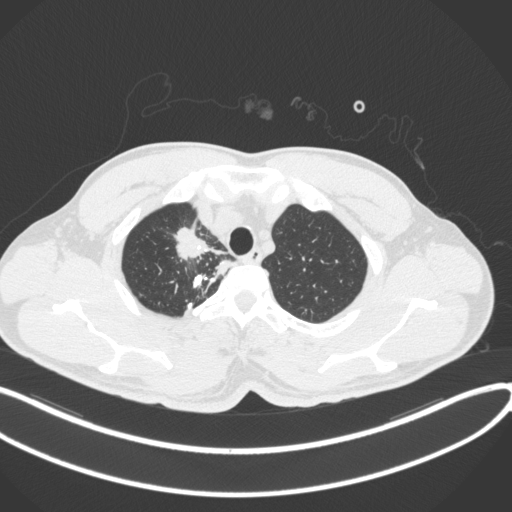
Chest CT, one axial slice; slice 325 of 391 in the series (ordered by position); reconstruction kernel B31f; 120 kVp; lung window (W 1500 / L -600 HU); 512 × 512 image matrix. Male patient, age 48 years. Case-level facts recorded for this patient, not image findings: clinical TNM (as recorded): T1c N1 M1.
Outlined on this slice (bounding box drawn by a radiologist):
- lung tumour (recorded histology: adenocarcinoma): box from (x=171, y=221) to (x=229, y=261) px